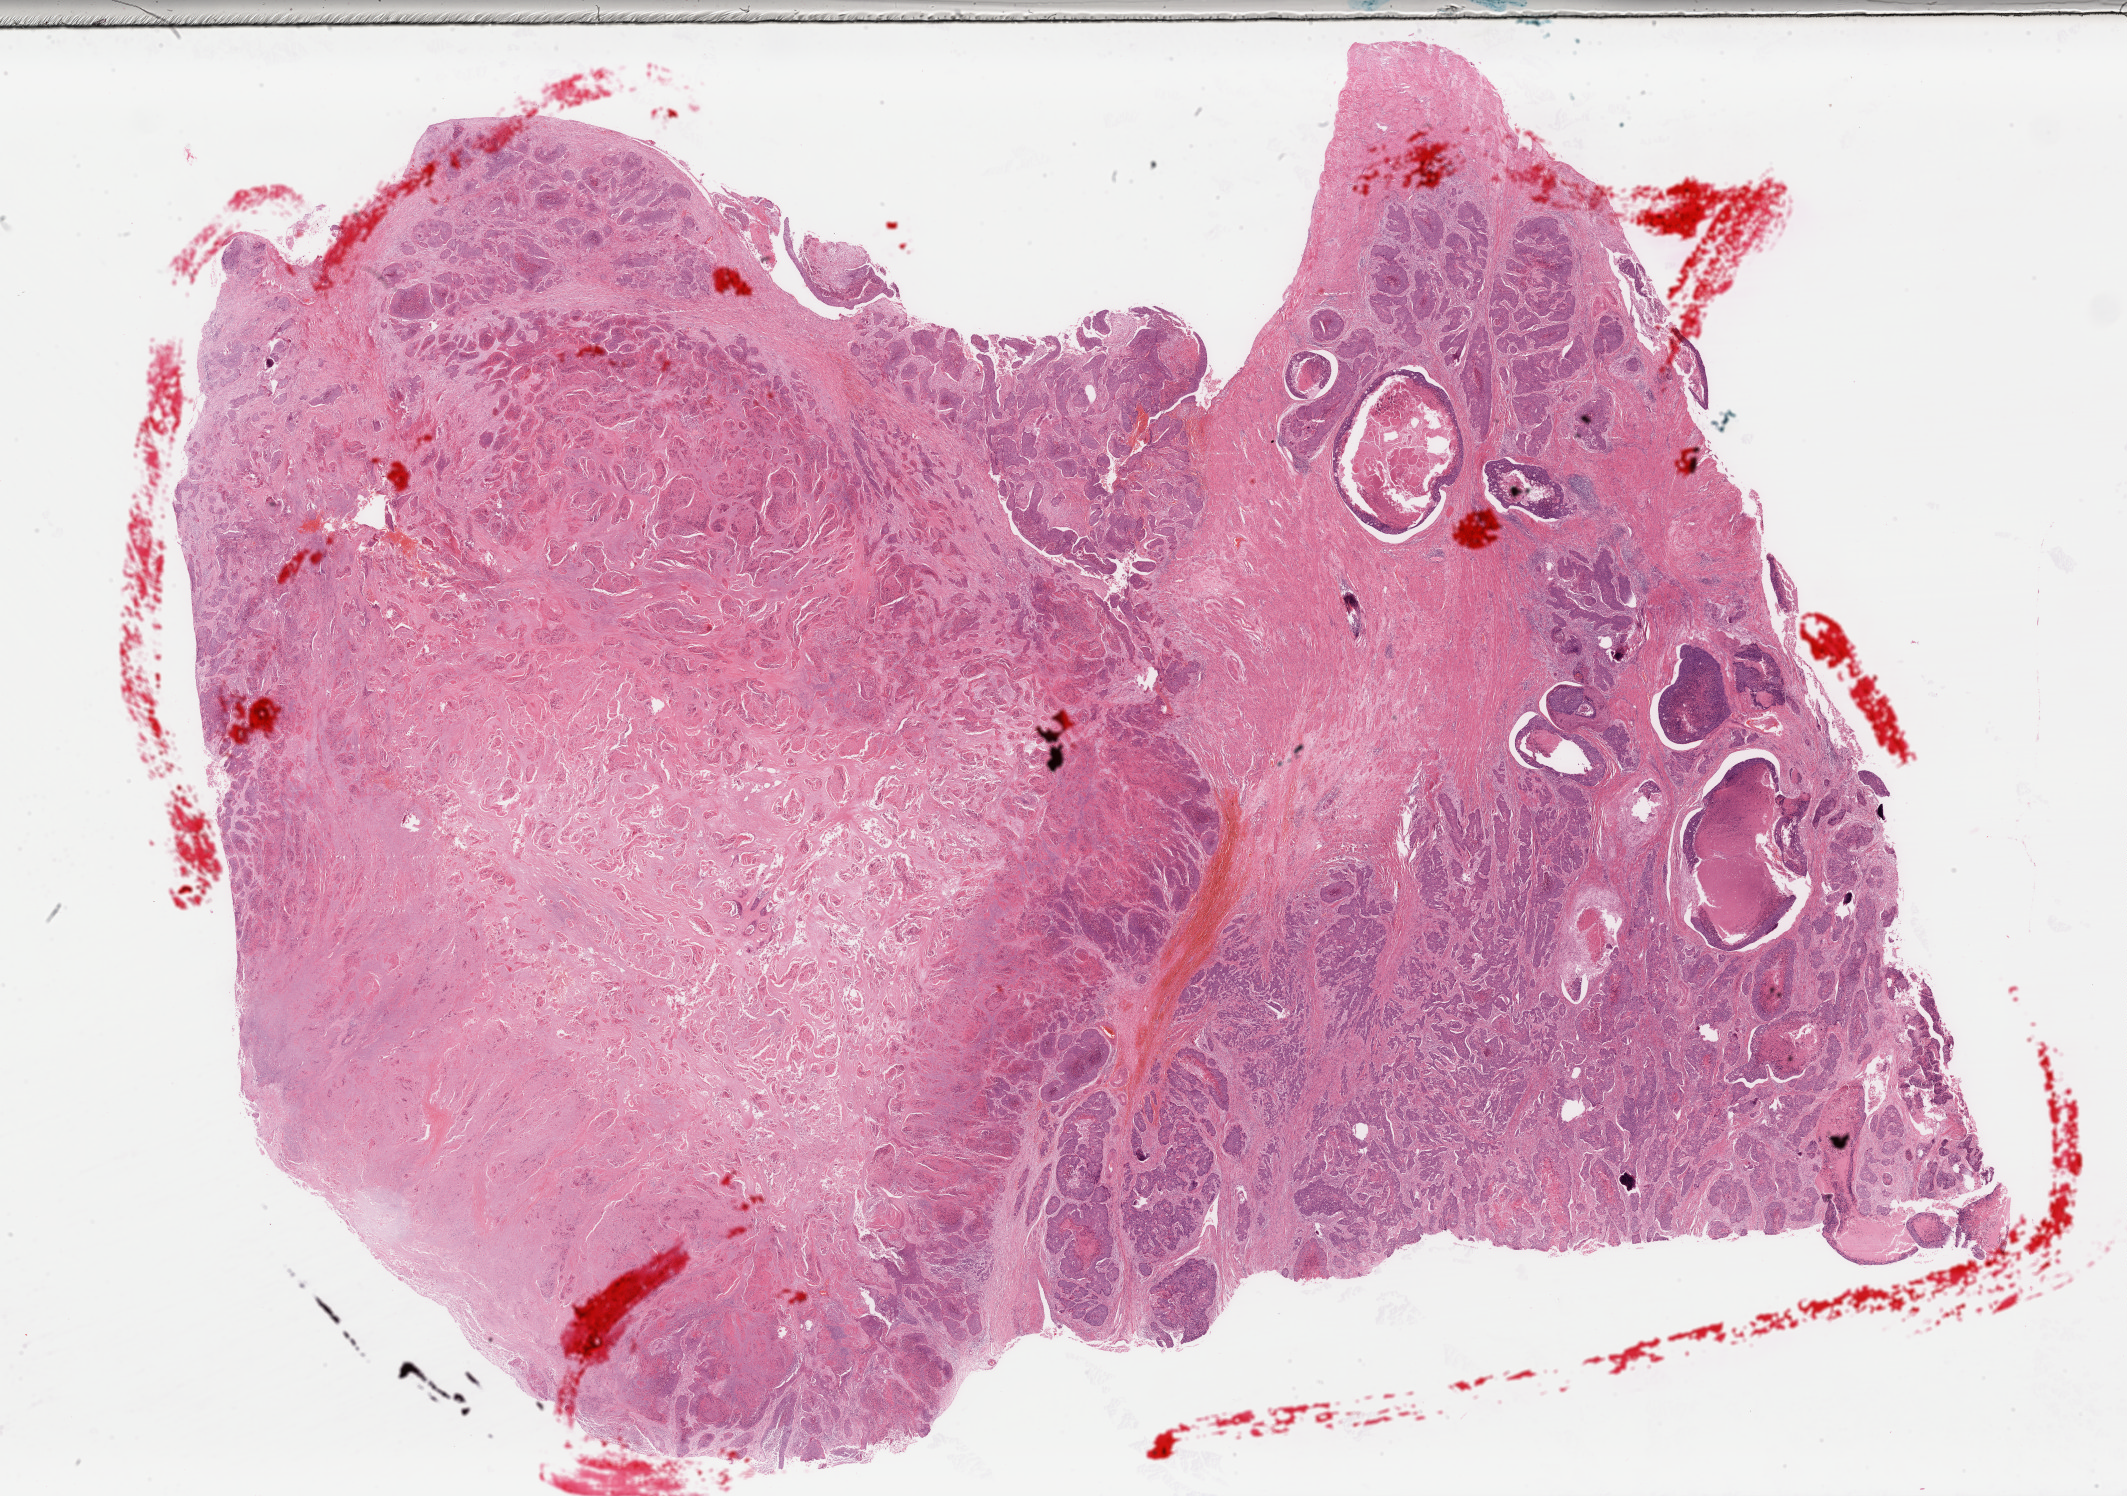
Digitized H&E tissue section (whole slide) — shown as a low-resolution overview of the whole scanned area (about 33.6 x 23.6 mm, from a 40x scan). FFPE section. Primary tumour sample from the cervix. Female patient; age at initial diagnosis 45 years. Histologic grade: G2 (moderately differentiated).
• FIGO stage: IVA
• histologic diagnosis: Squamous cell carcinoma, large cell, nonkeratinizing, NOS (cervix uteri)